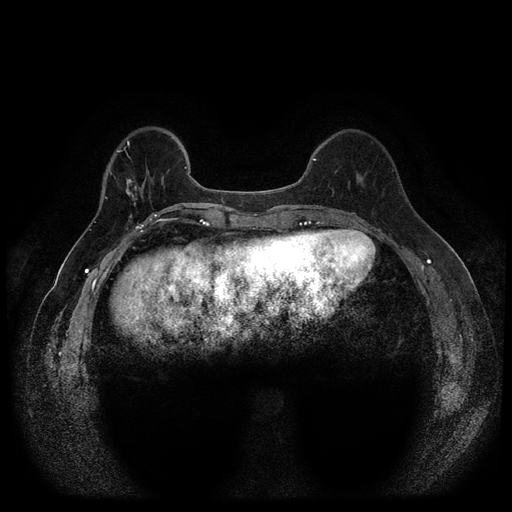
Breast MRI (dynamic contrast-enhanced, multi-phase), one axial slice. Slice 30 of 116 in the series (ordered by position). Dynamic contrast-enhanced series, time point 2 of 5 at this slice position (early post-contrast). 1.5 T. TE 2.6 ms, TR 5.4 ms. 512 × 512 image matrix, field of view 340 × 340 mm. Female patient, age 56 years.
Outlined on this slice (semi-automatic segmentation, software-assisted and operator-edited):
- breast lesion (labelled 'tumour' in the annotation; benign lesions carry a separate 'benign' label): bounding box <122,167,153,215> (left, top, right, bottom; pixels)